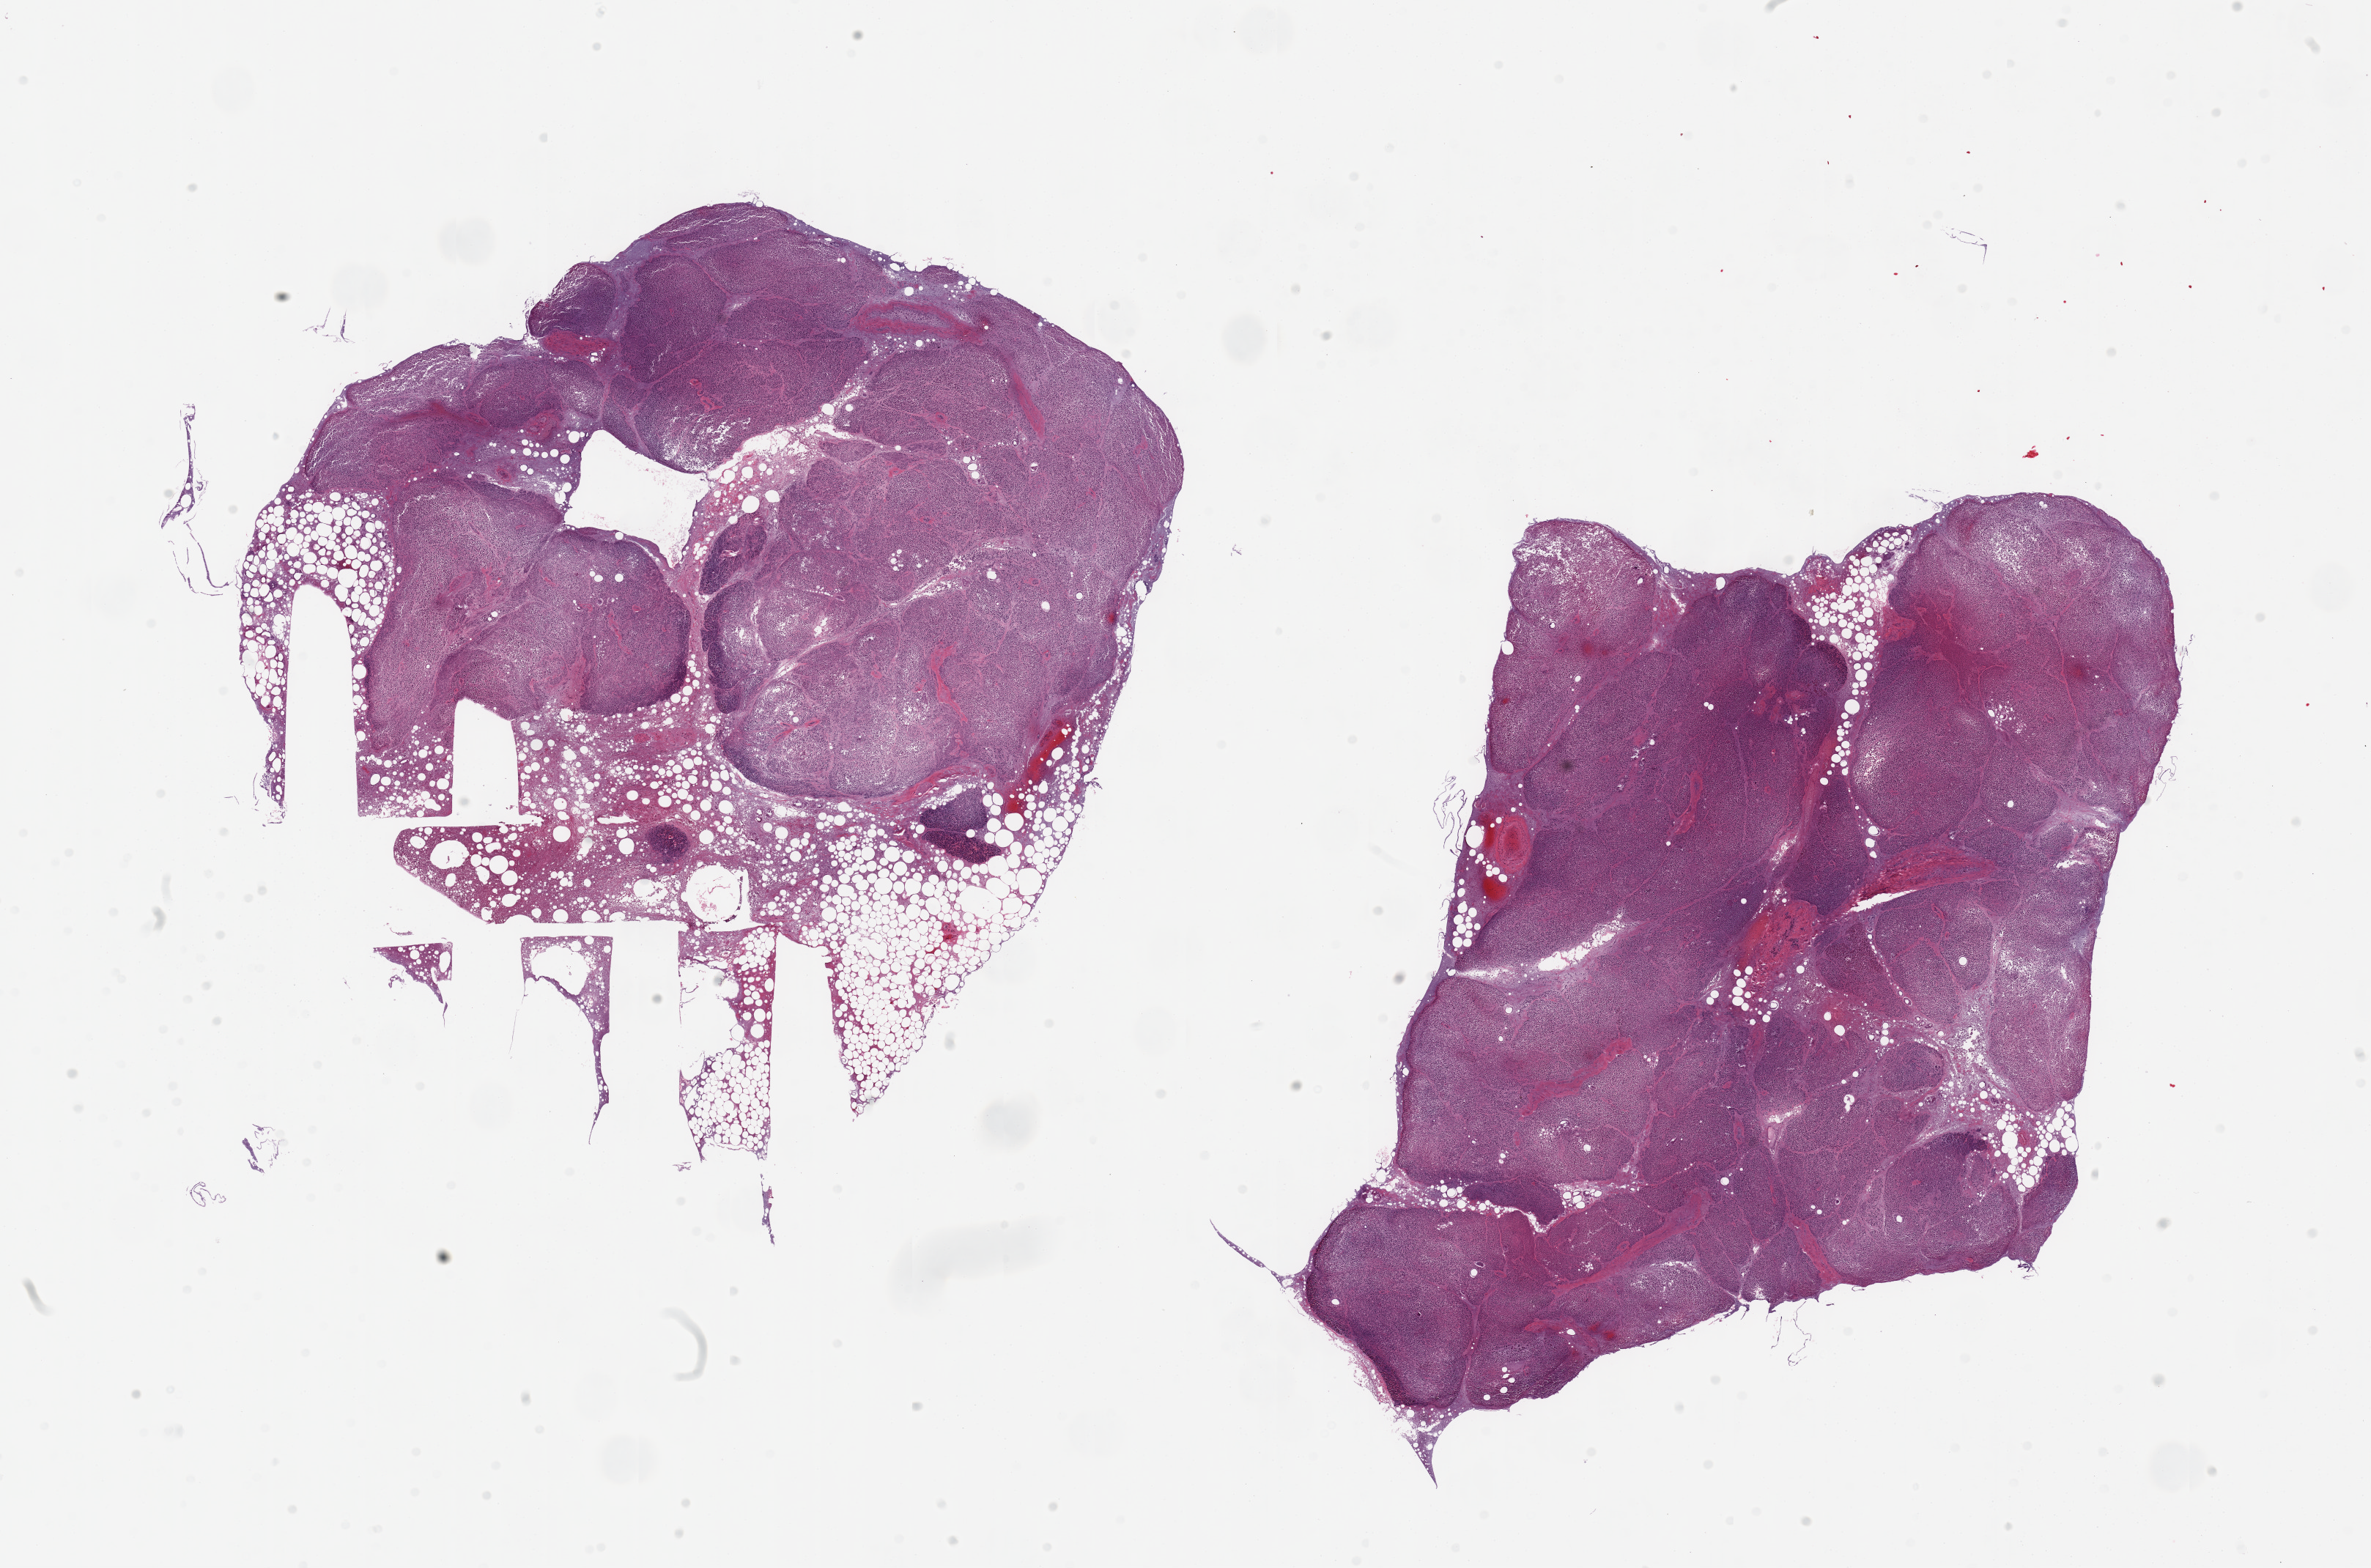
Digitized hematoxylin and eosin (H&E)-stained section, brightfield — whole scanned area (about 25.6 x 16.9 mm) shown as a low-resolution overview; PAXgene-fixed paraffin-embedded (PFPE) section; section of pancreas (target tissue); tissue donor sample. Donor: male.
Review note (as recorded): 2 pieces, severely autolyzed.